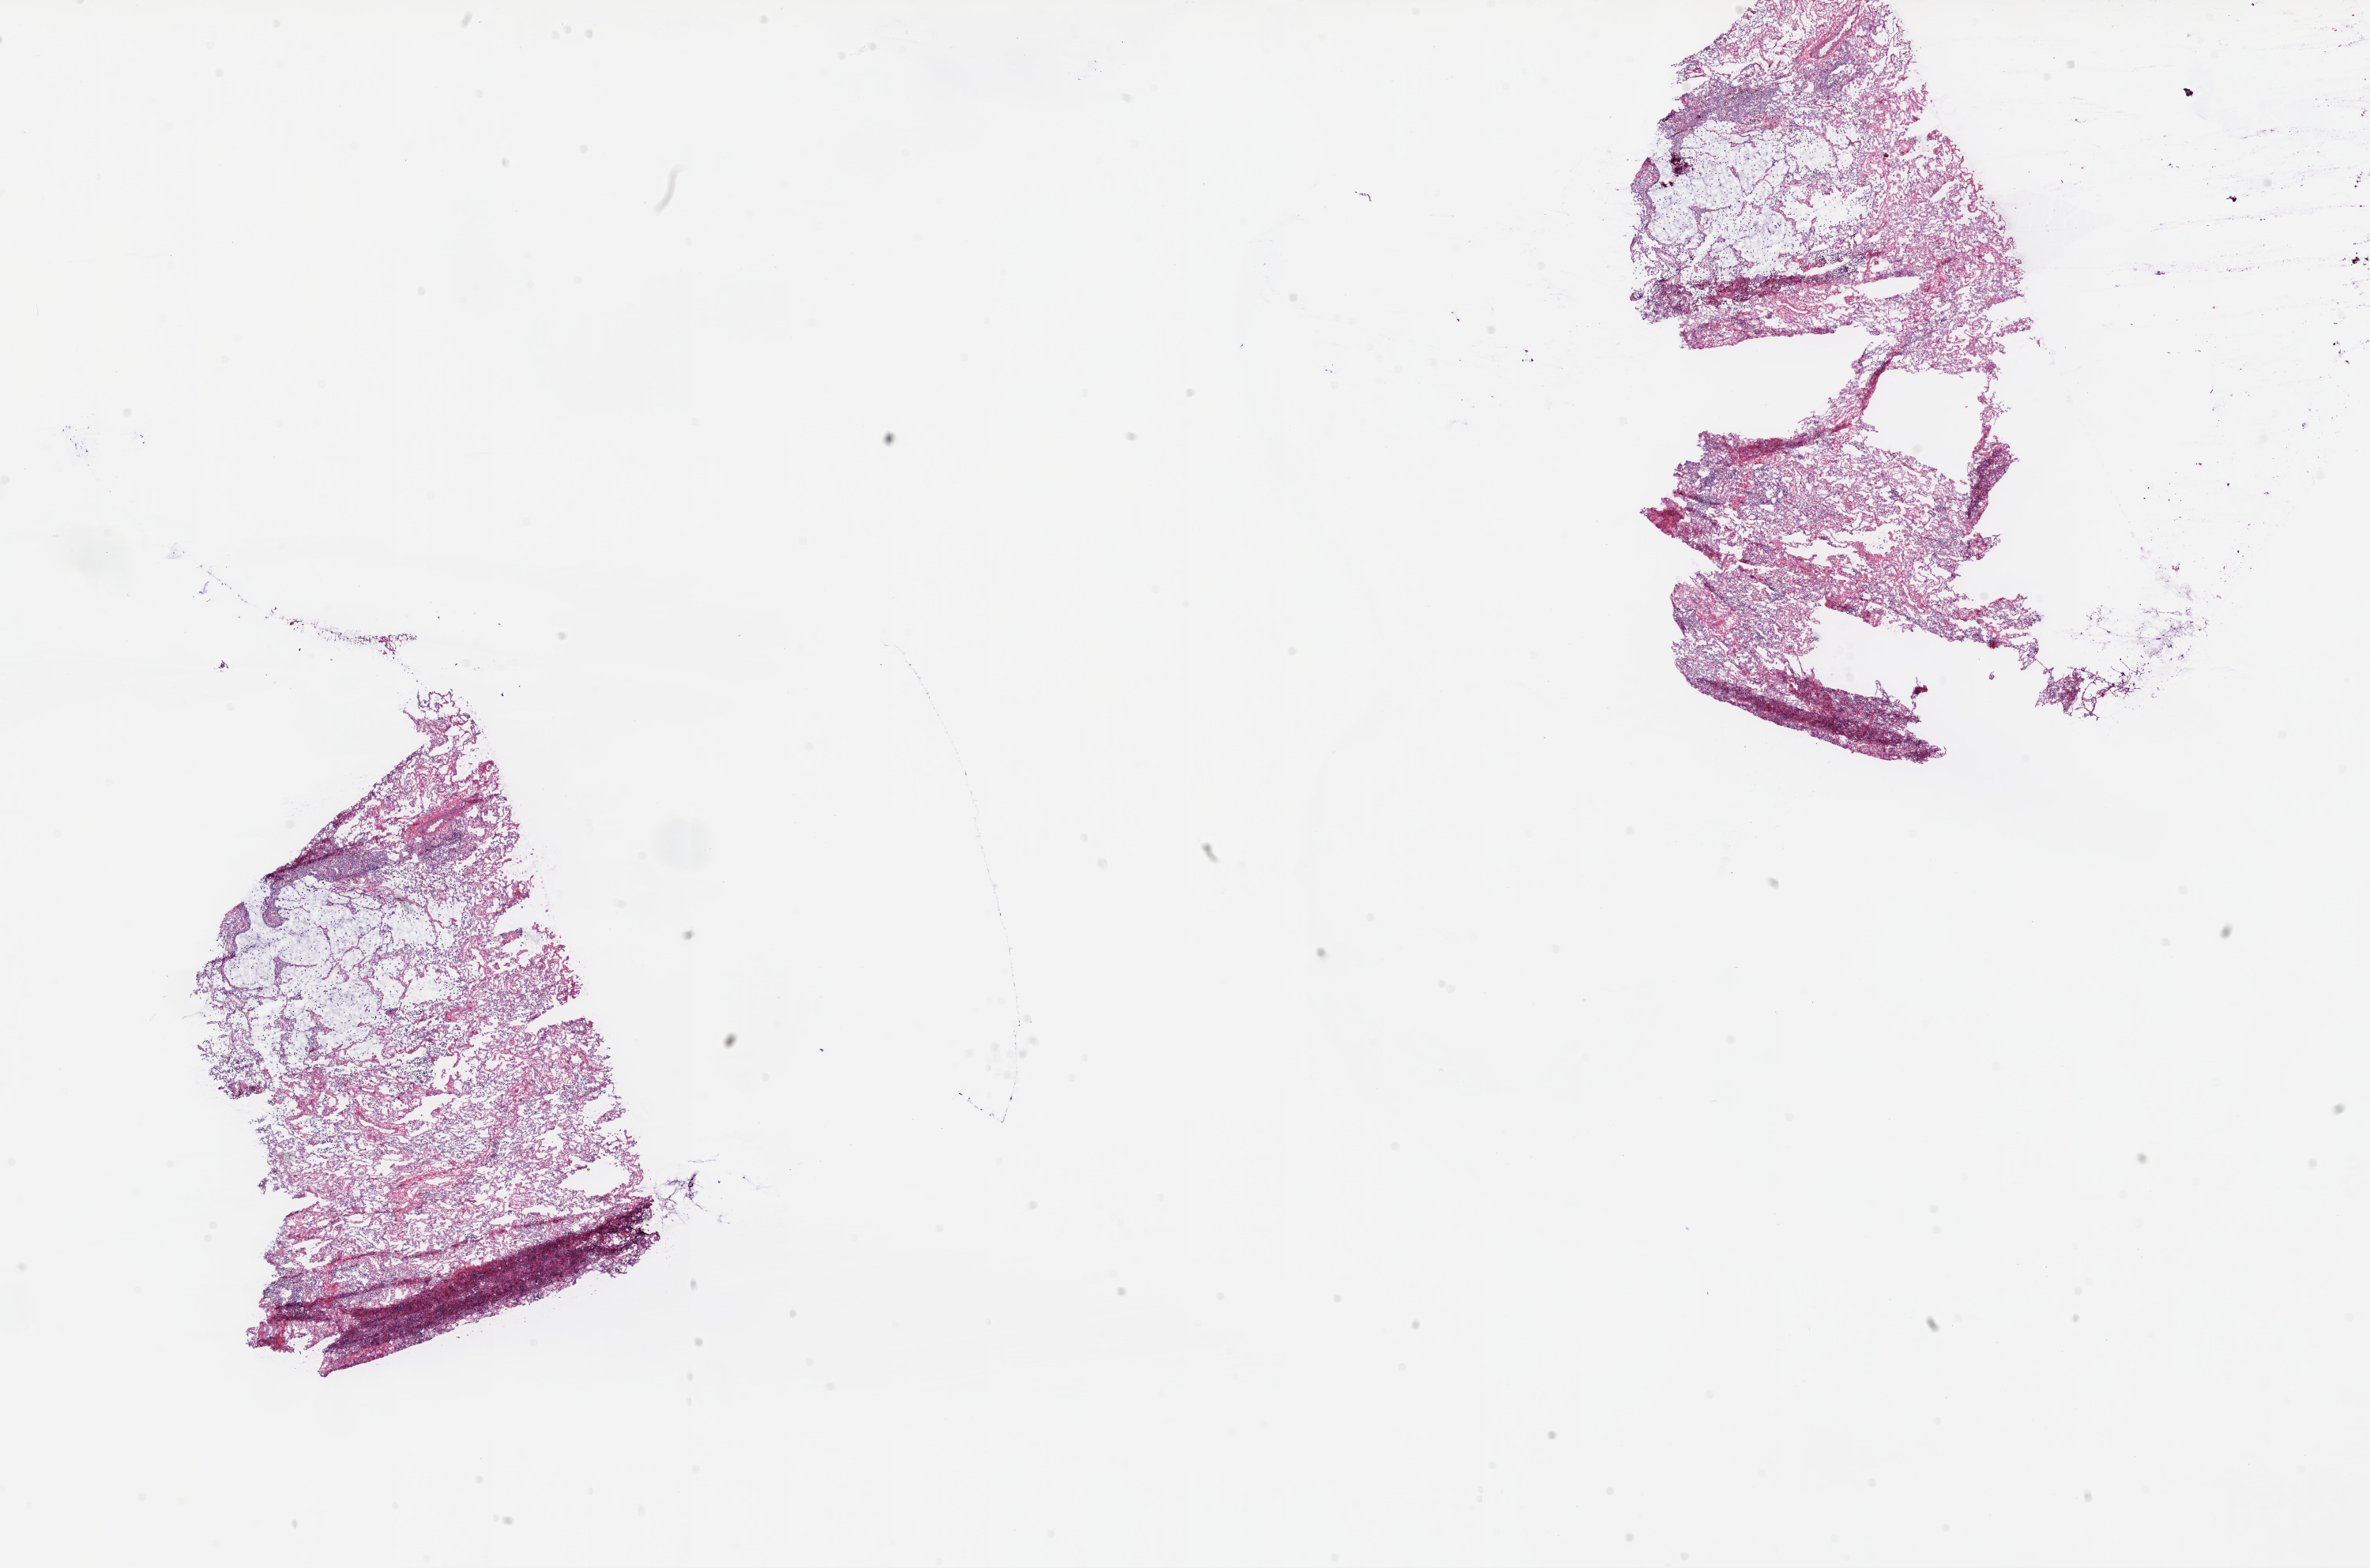
H&E-stained whole-slide image, a low-resolution overview of the entire scanned area, about 24.1 x 15.9 mm (slide scanned at 20x), frozen section from the bottom of the tissue portion, solid tissue normal (non-tumour tissue) sample from the lung. Female, age 63 years at initial diagnosis.
This section: solid tissue normal sample (biorepository sample class). Patient diagnosis: Squamous cell carcinoma, NOS (upper lobe, lung).